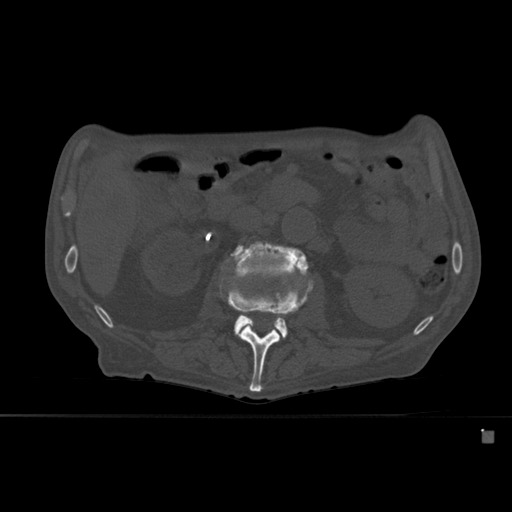
CT including the spine, one axial slice; position 227 of 527 along the scan axis; bone window (W 1800 / L 400 HU); 1.5 mm slice thickness; 512 × 512 image matrix, field of view 373 × 373 mm. Male patient, age 78 years. From the clinical record (not read from this slice): primary cancer: prostate.
Annotated regions visible in this slice (semi-automatically segmented with operator editing):
- L2 vertebra: bounding box <227,277,313,392> (left, top, right, bottom; pixels)
- L3 vertebra: <229,241,309,338>